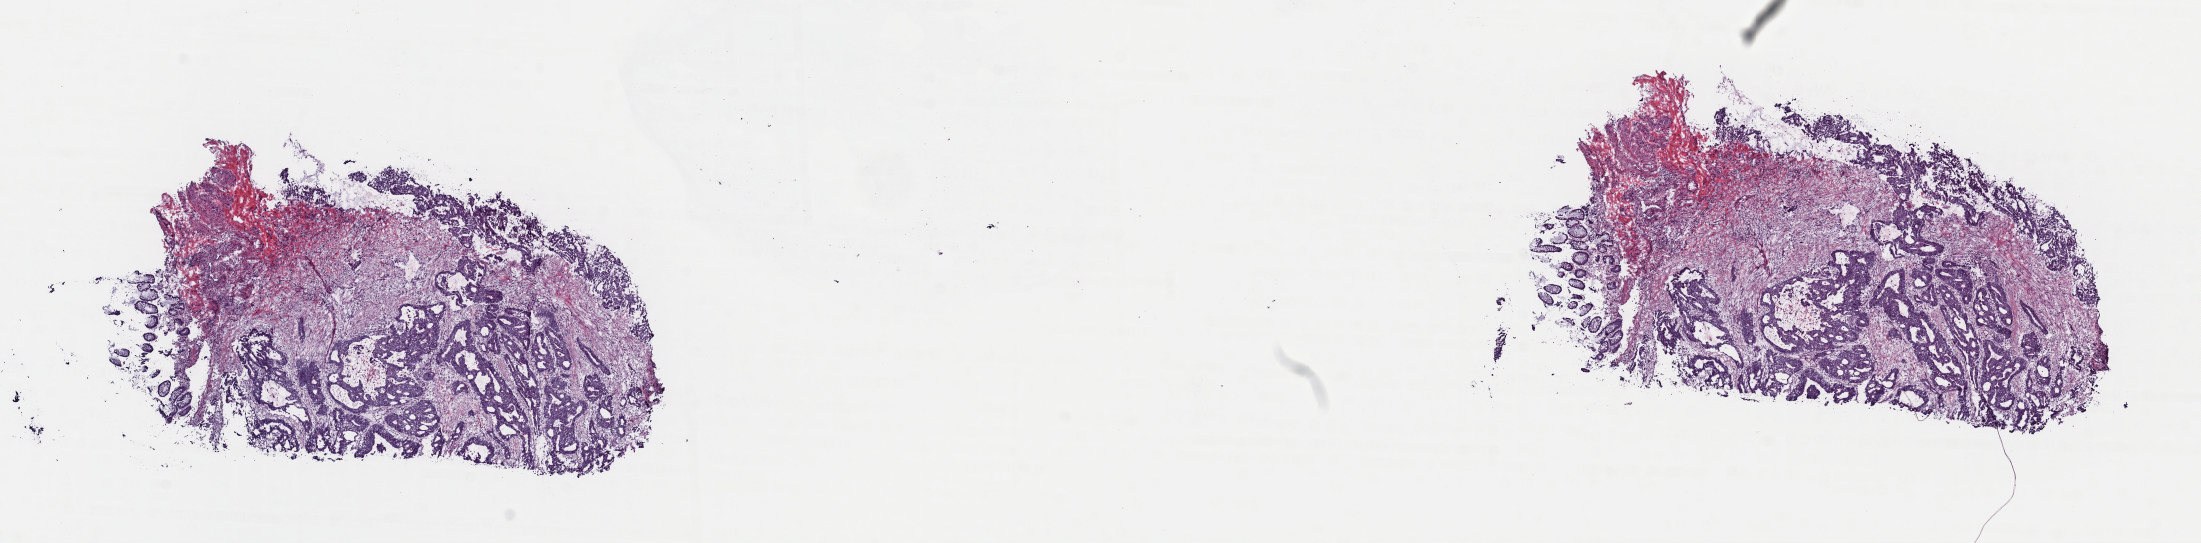
Whole-slide histology image, H&E, low-resolution overview of the scanned area, about 17.4 x 4.3 mm; frozen section from the top of the tissue portion; colon, primary tumour sample. Male patient; age at initial diagnosis 51 years. Composition of this section per pathologist review: tumour cells 85%, tumour nuclei 65%, normal cells 15%, stromal cells 0%, necrosis 0%. Infiltration values recorded for this section: lymphocyte infiltration 5%, monocyte infiltration 0%, neutrophil infiltration 0%.
• diagnosis: Adenocarcinoma, NOS (ascending colon)
• AJCC pathologic stage: I (7th edition)